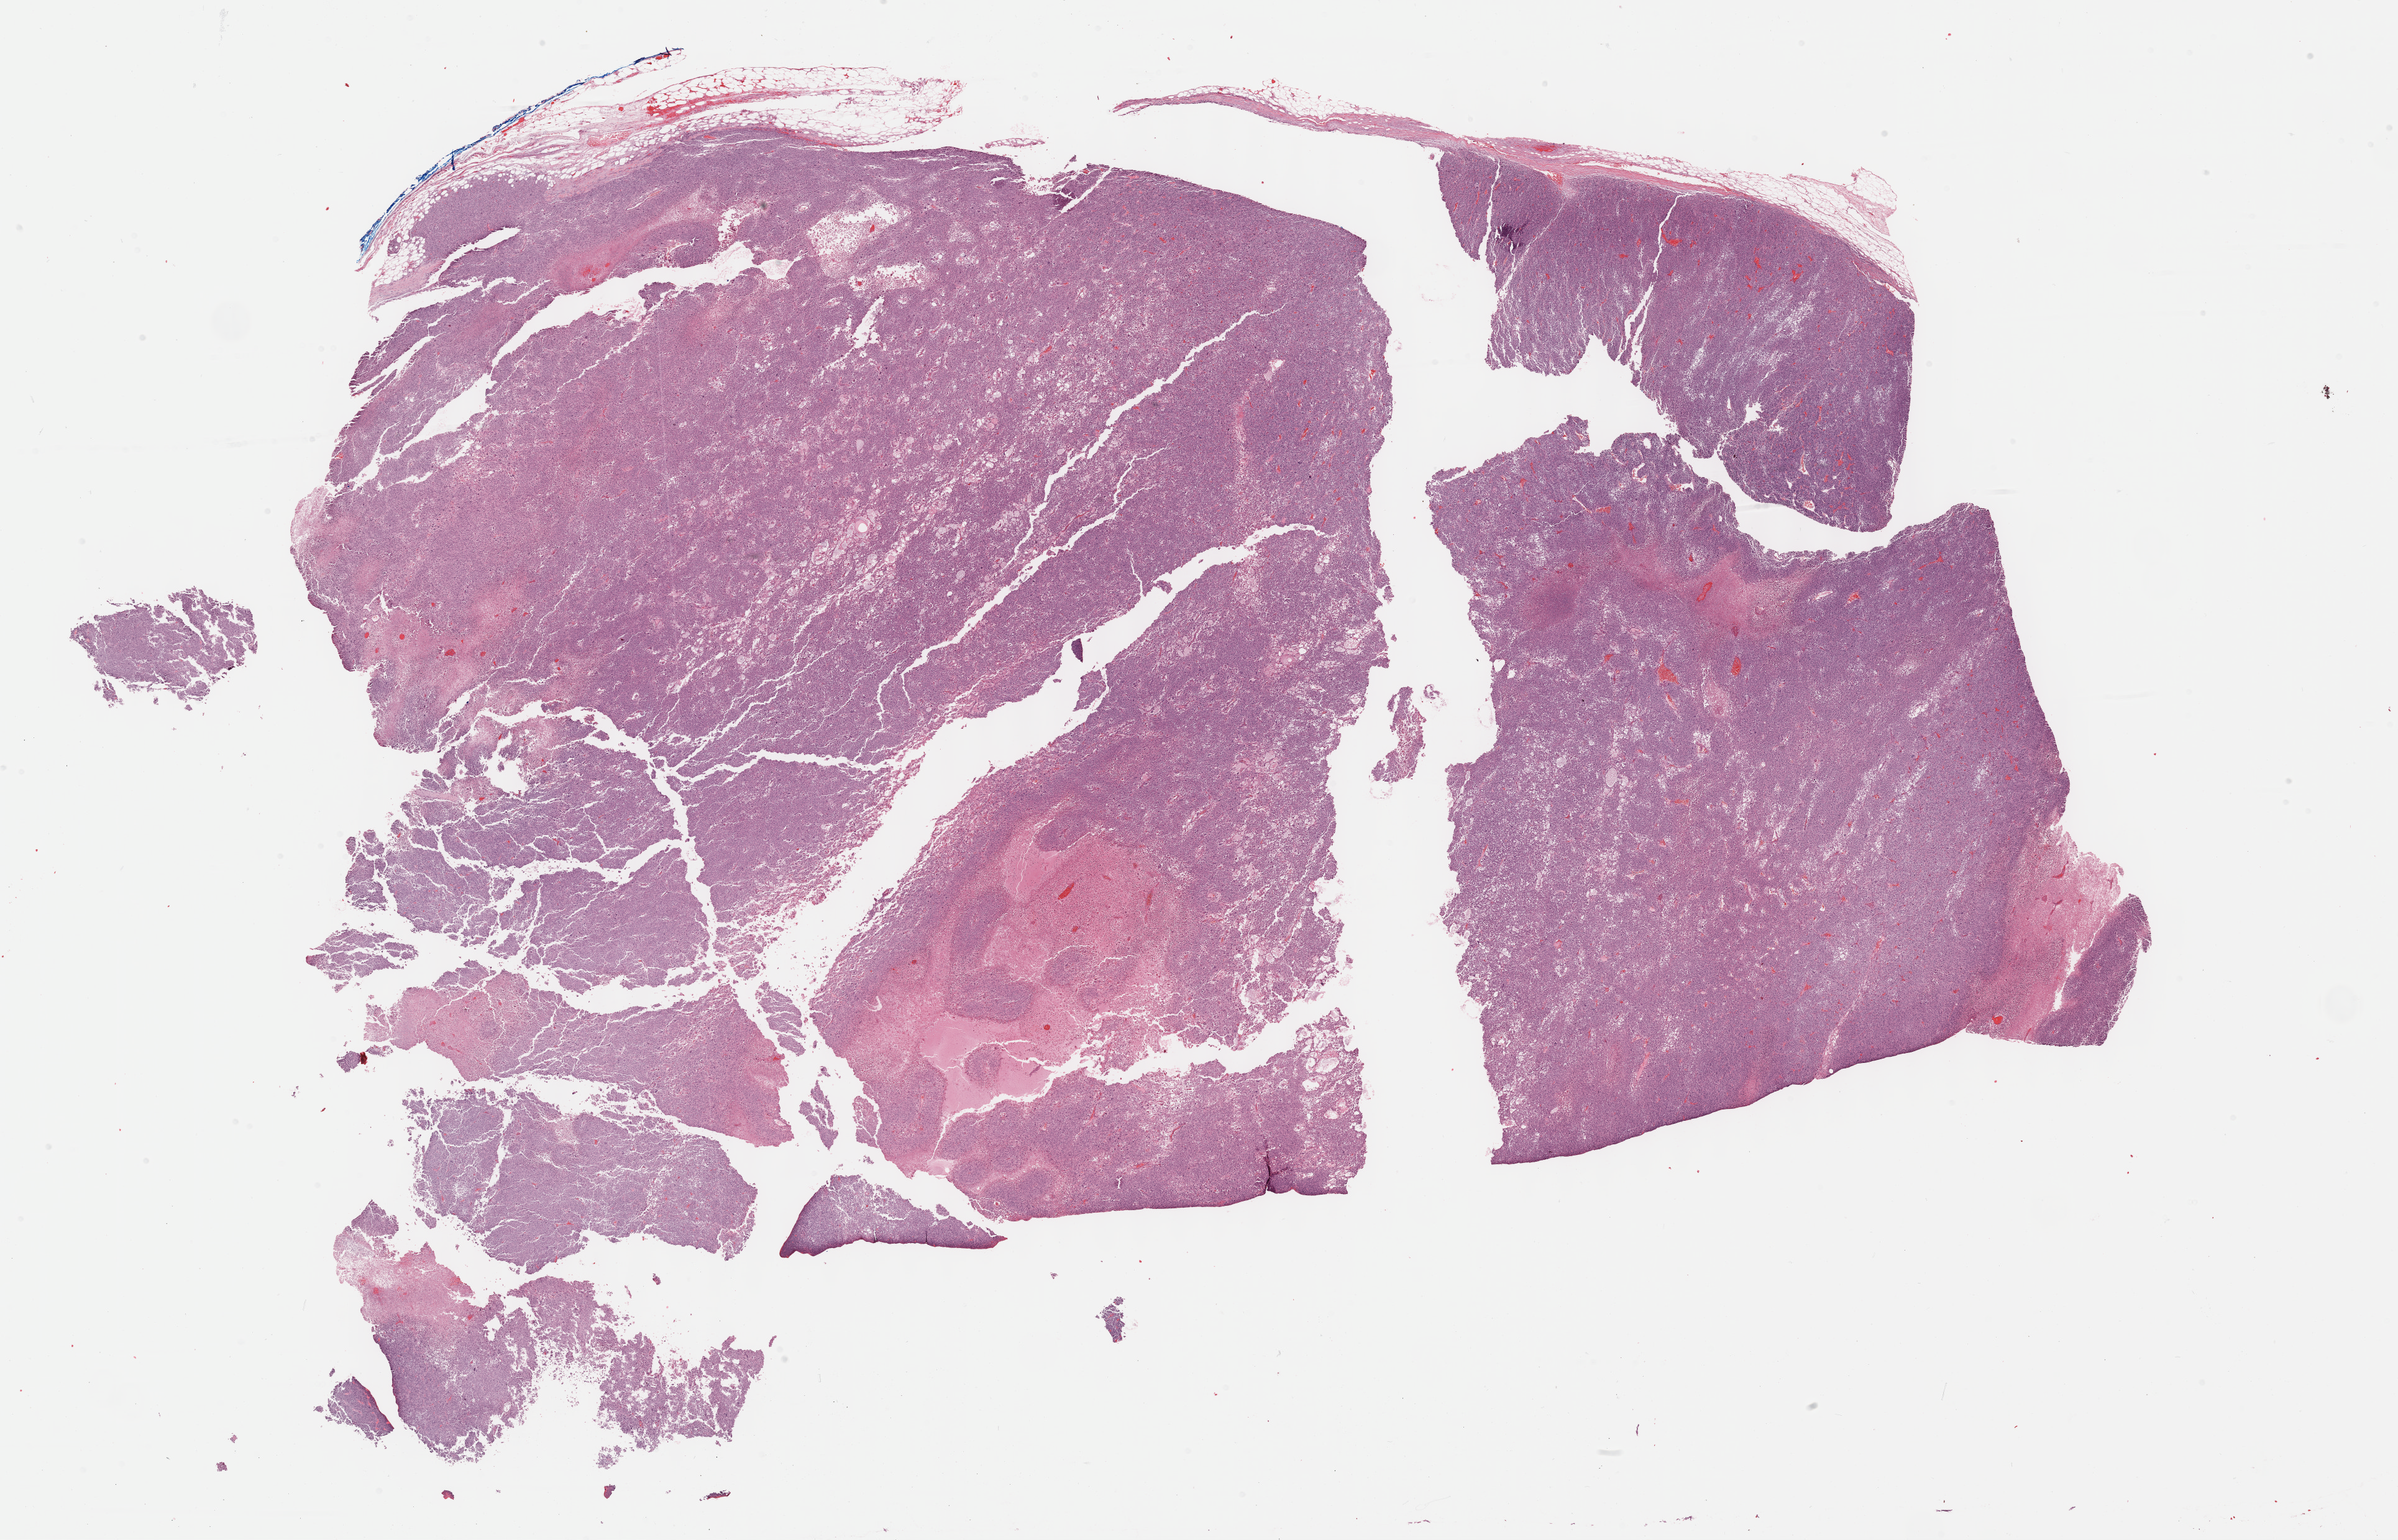
Digitized H&E tissue section (whole slide) — a low-resolution overview of the entire scanned area, about 31.2 x 20.0 mm; FFPE section; primary tumour sample from the retroperitoneum and peritoneum. Male patient; age at initial diagnosis 60 years.
Histologic diagnosis: Dedifferentiated liposarcoma (retroperitoneum).